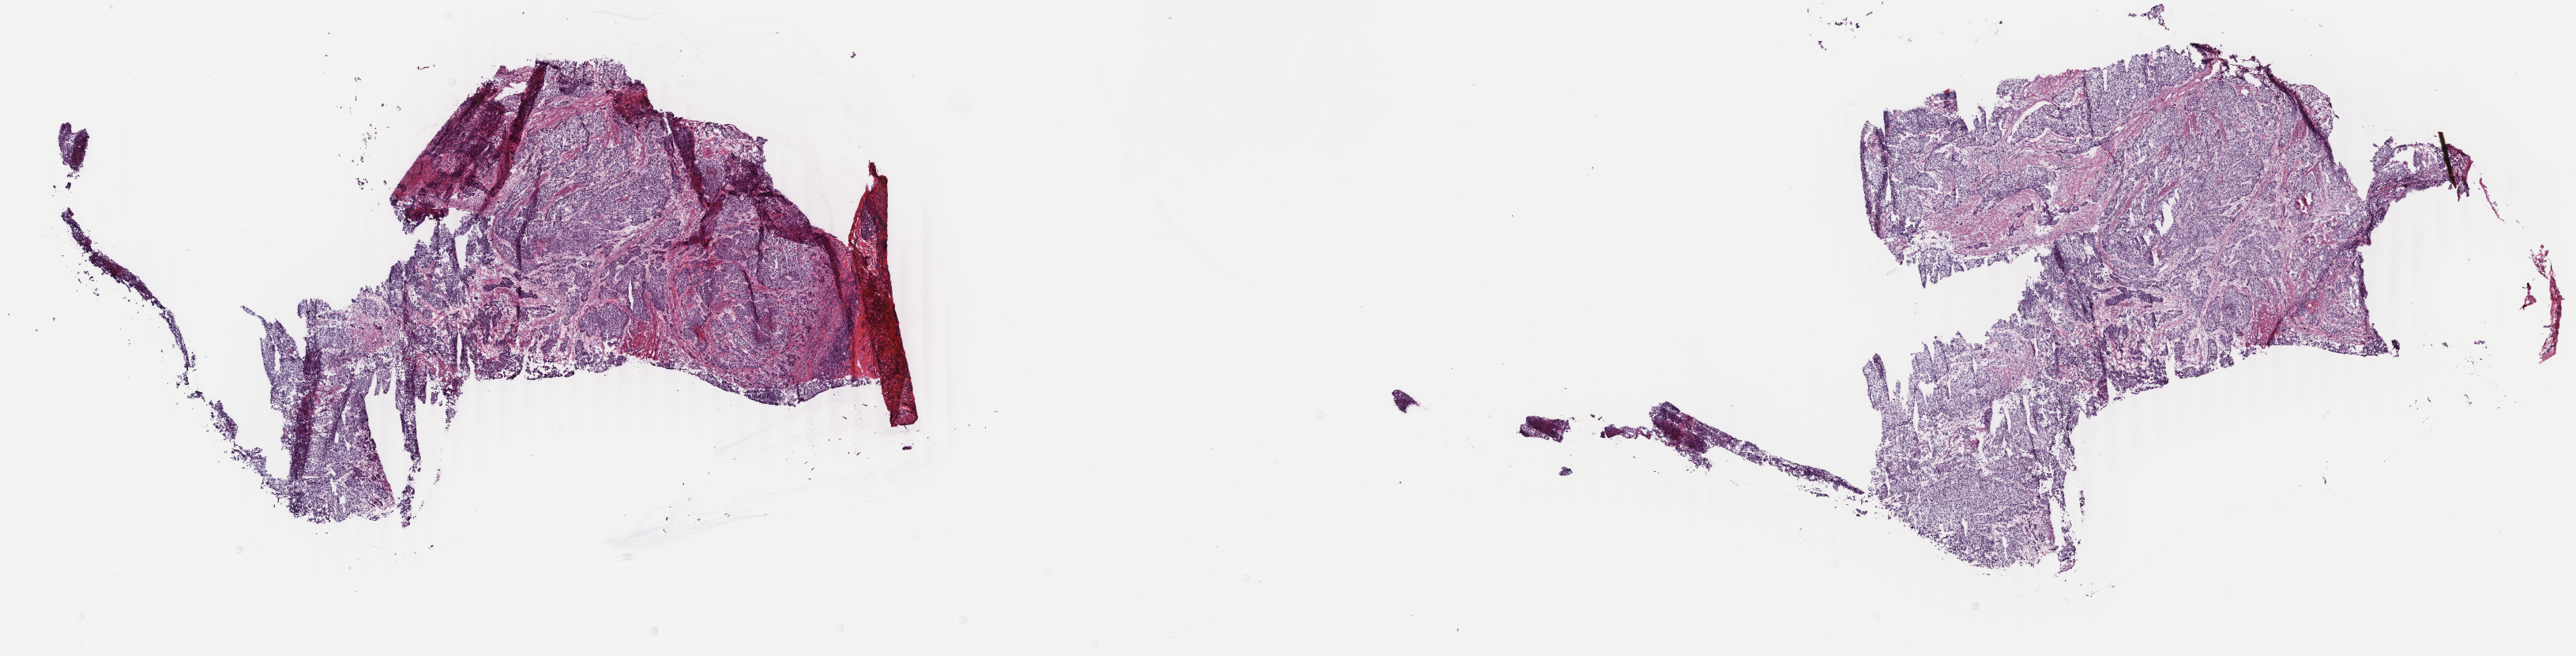
H&E-stained whole-slide image — whole scanned area (about 25.9 x 6.6 mm) shown as a low-resolution overview, frozen section, sample: primary tumour, bladder. Female patient; age at initial diagnosis 82 years. Histologic grade: high grade. Slide review estimates, as recorded: tumour cells 70%, tumour nuclei 70%, normal cells 9%, stromal cells 18%, necrosis 3%. Inflammatory infiltration, as recorded: lymphocyte infiltration 3%, monocyte infiltration 0%, neutrophil infiltration 0%.
• TNM: T3b N0 M0
• AJCC pathologic stage: III (6th edition)
• diagnosis: Transitional cell carcinoma